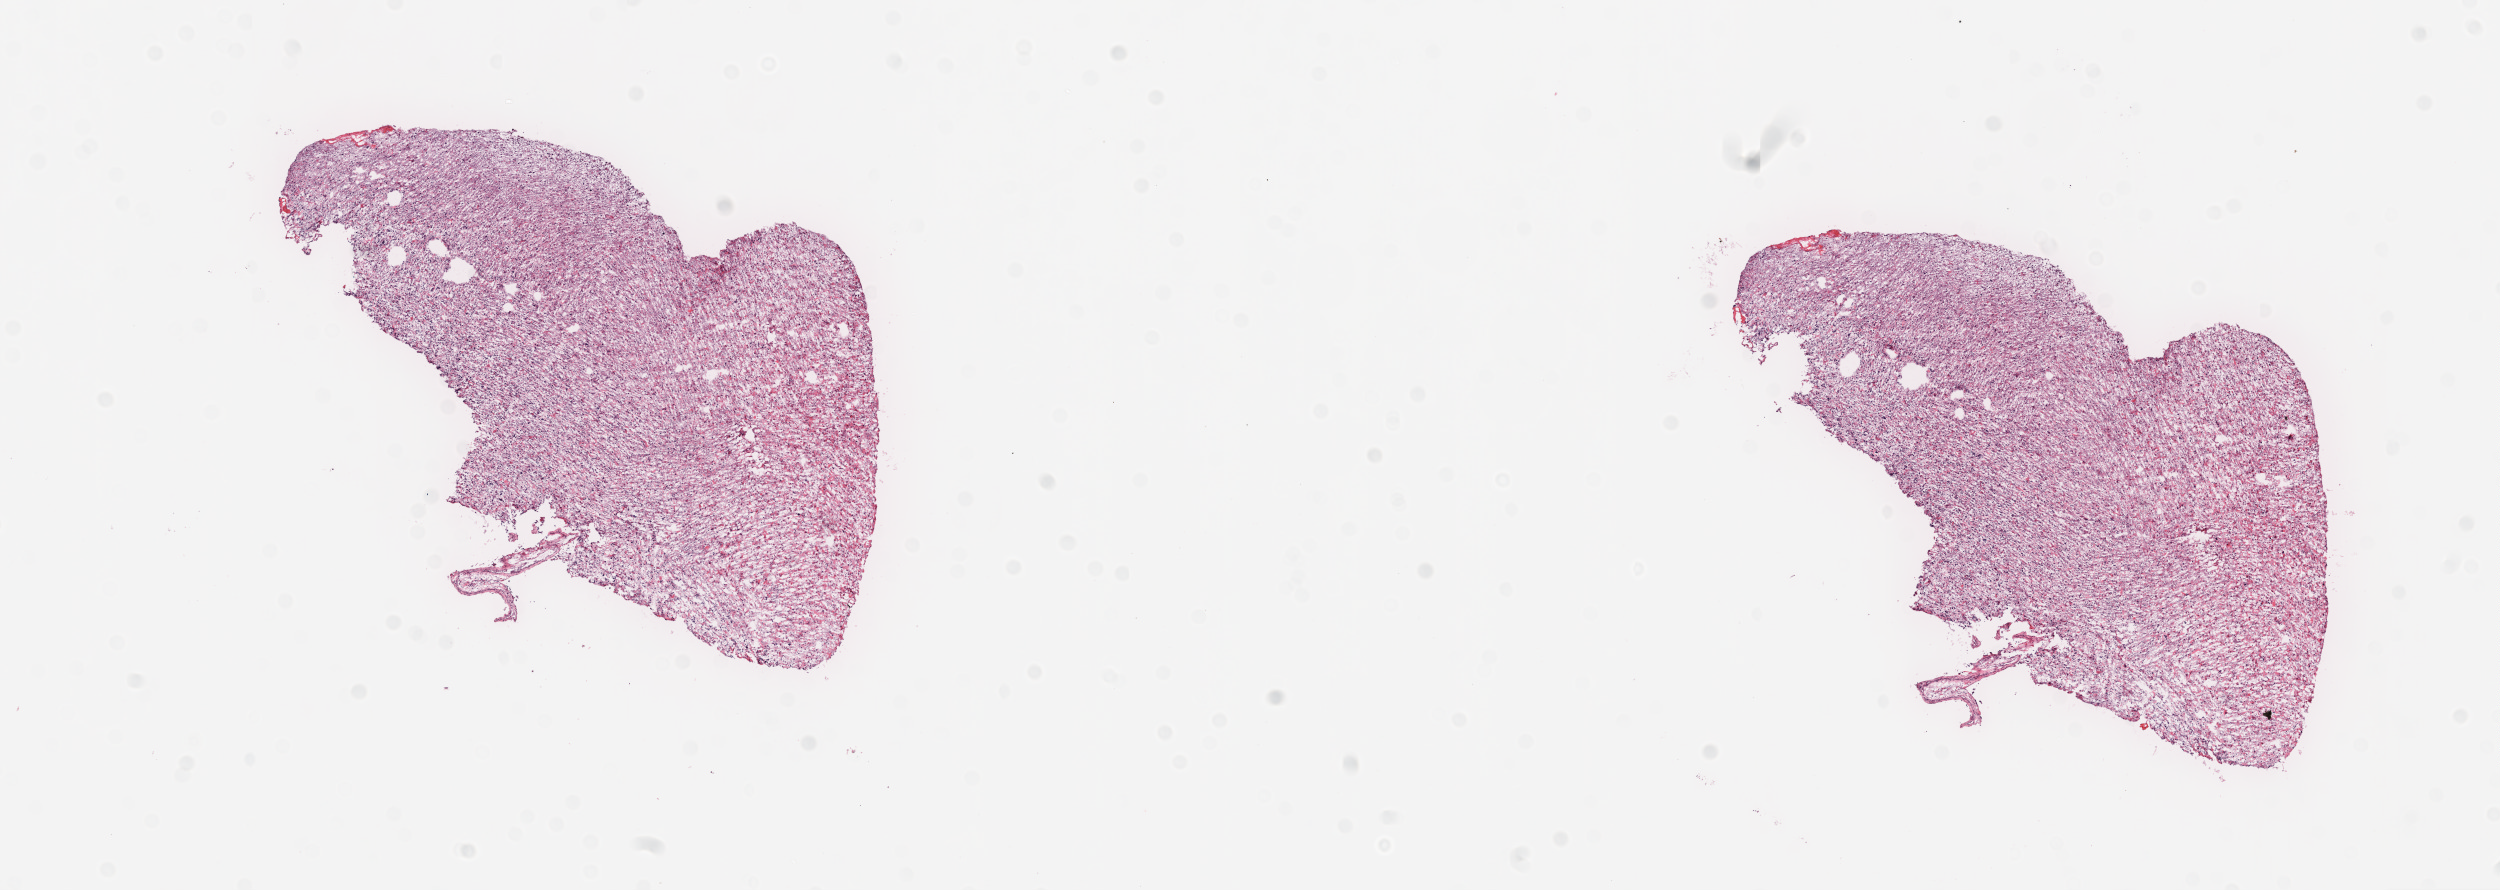
Whole-slide histology image, H&E — shown as a low-resolution overview of the whole scanned area (about 20.1 x 7.1 mm, slide scanned at 20x); frozen section from the top of the tissue portion; primary tumour sample from the brain. Male, age 60 years at initial diagnosis. Slide review estimates, as recorded: tumour cells 100%, tumour nuclei 85%.
Histologic diagnosis: Glioblastoma.